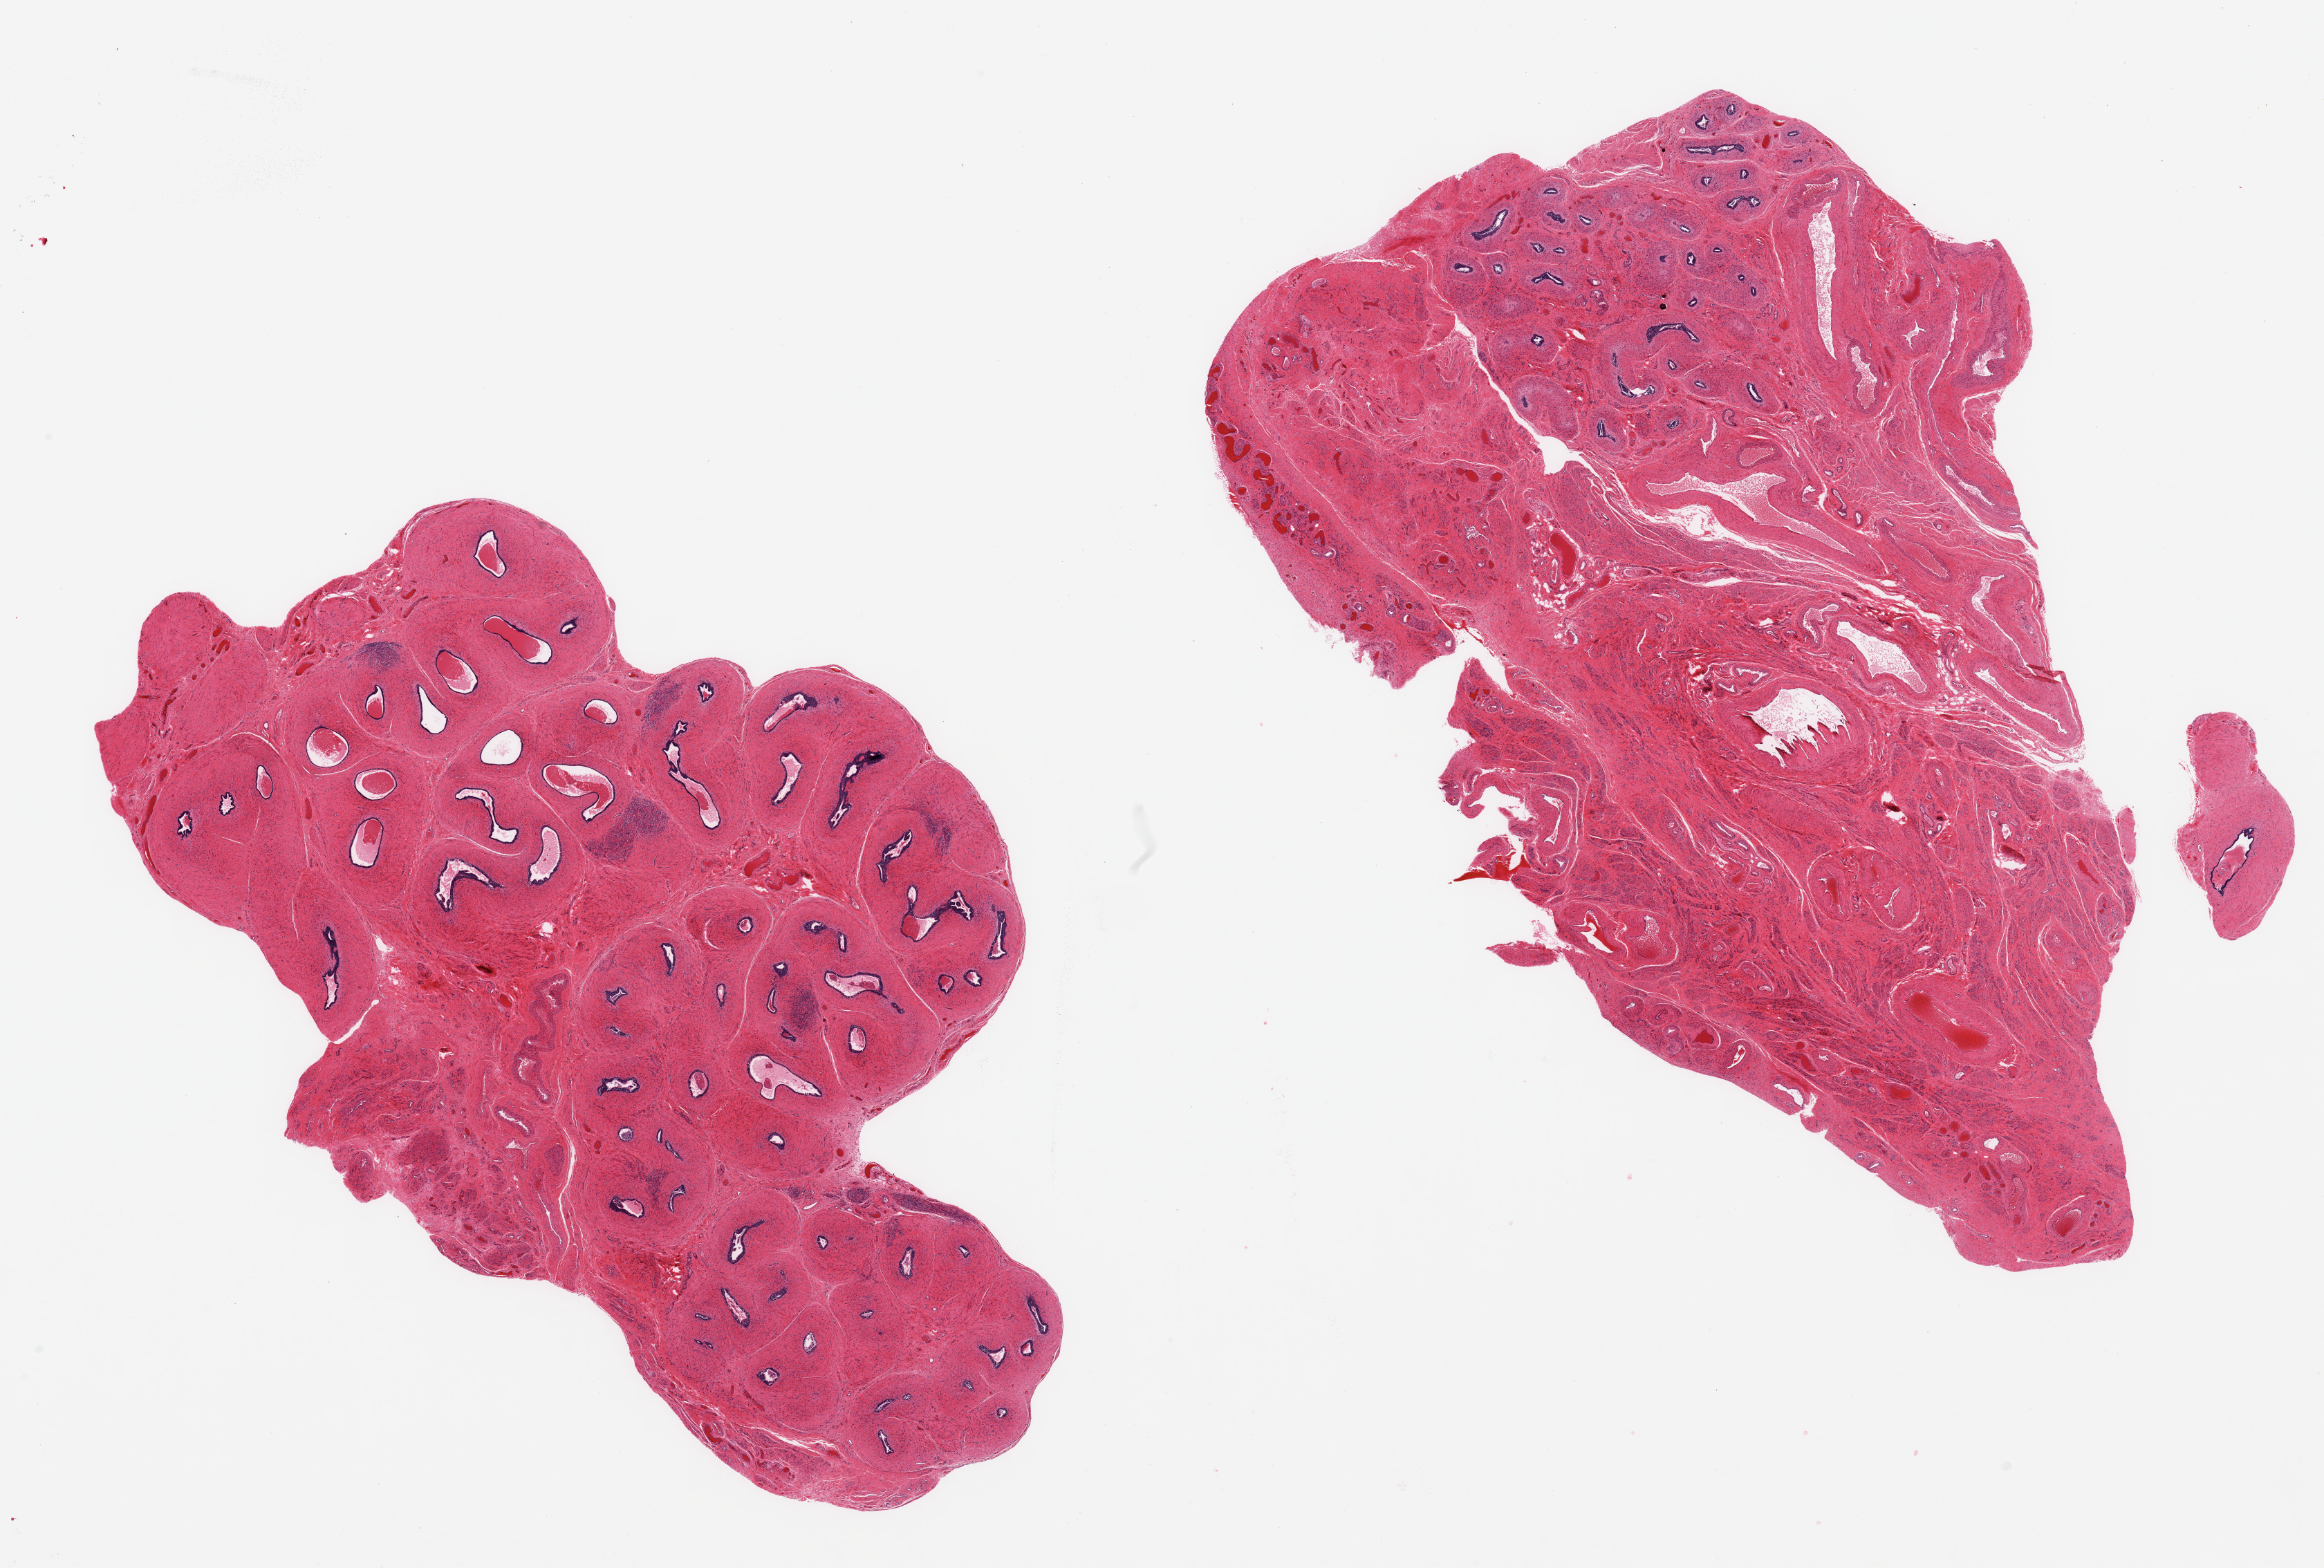
Haematoxylin and eosin whole-slide image, shown as a low-resolution overview of the whole scanned area (about 26.6 x 17.9 mm, acquisition: 20x scan). PAXgene-fixed paraffin-embedded (PFPE) section. Target tissue: testis. Donor tissue sample.
* review note (as recorded): 2 pieces: epididymis, no seminiferous tubules present